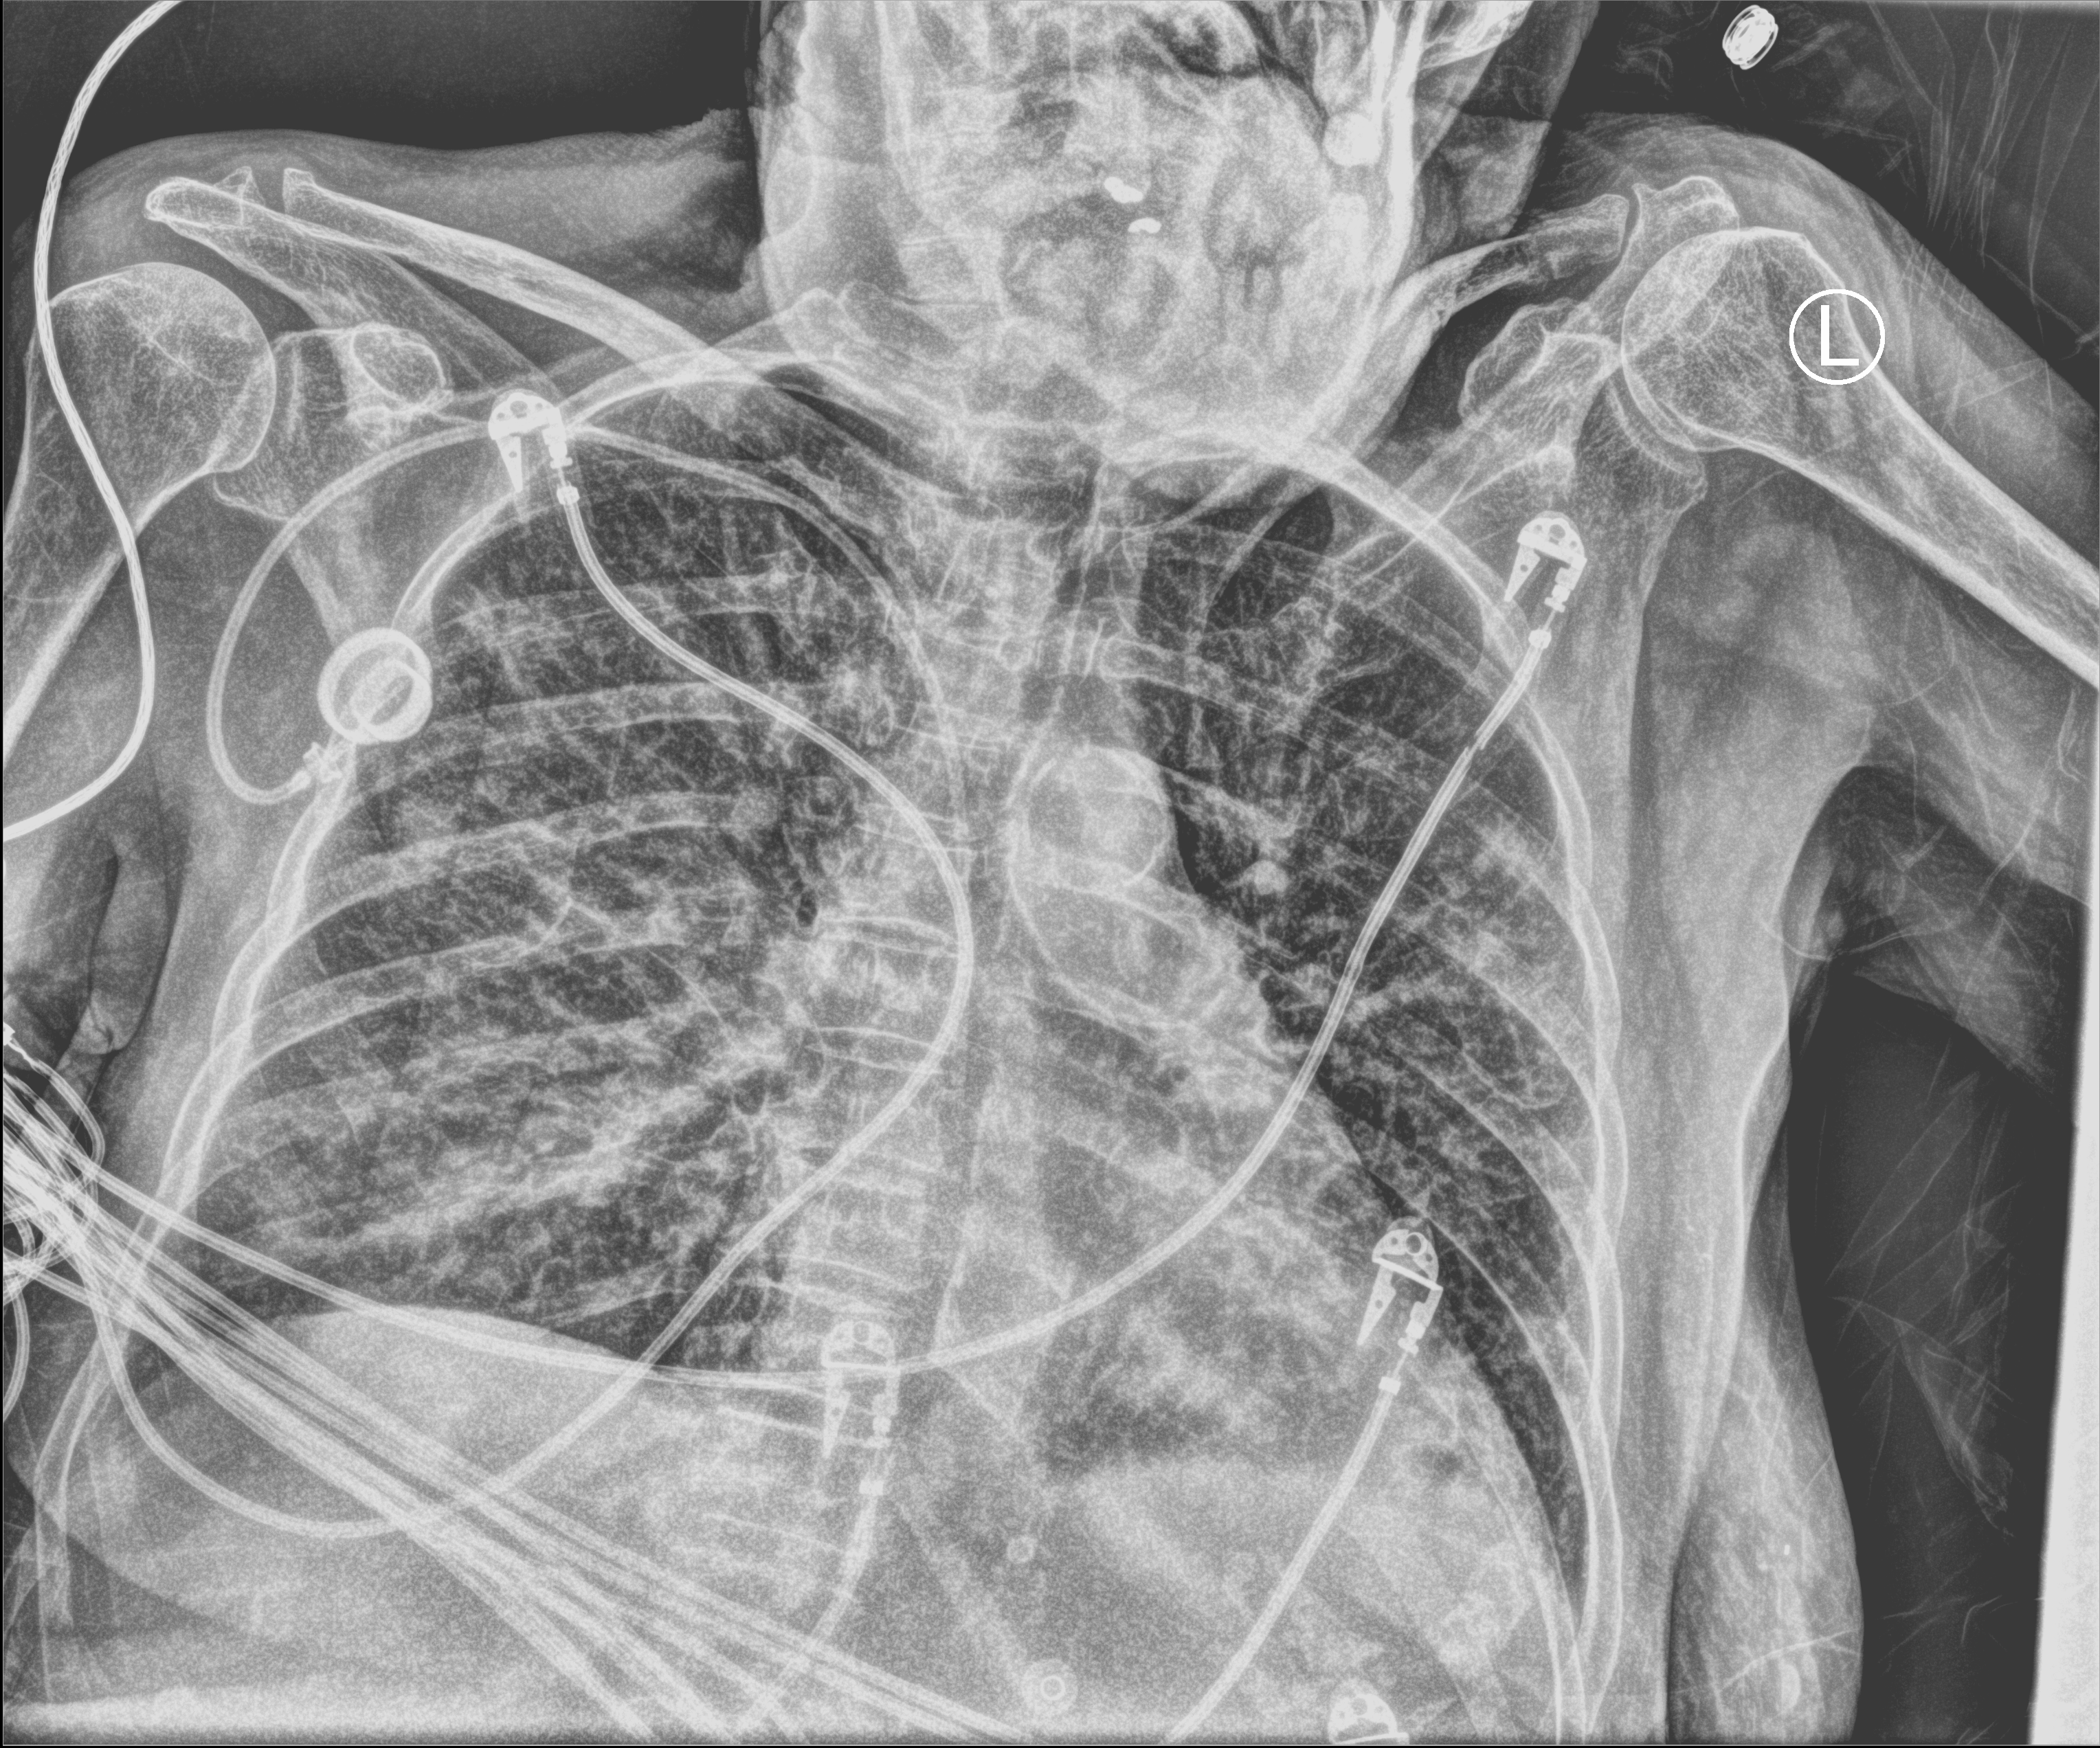
Chest X-ray (portable), anteroposterior (AP) projection. Female patient hospitalised with COVID-19, age 75–90 years.
From the hospital-stay record, not from the radiograph (when in the stay this image was taken is not recorded): admitted to intensive care during this hospital stay: yes.